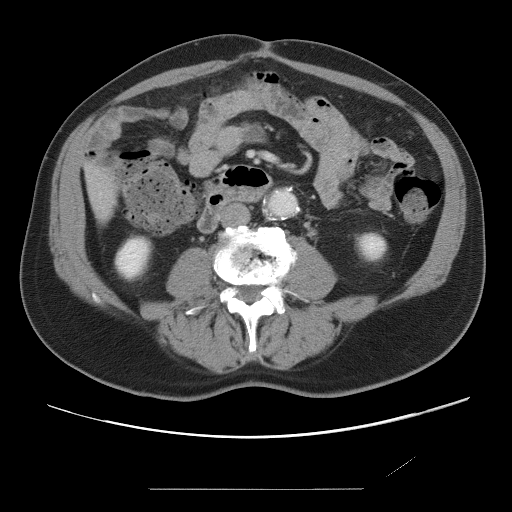
Contrast-enhanced abdominal CT, one axial slice. Position 9 of 87 along the scan axis. 120 kVp. Intravenous contrast given. Soft-tissue window (W 400 / L 40 HU). 5 mm slice thickness. 512 × 512 image matrix, field of view 406 × 406 mm. Male patient, age 74 years. From the clinical record (not read from this slice): diagnosis: colorectal cancer liver metastases, imaged before liver resection; multiple liver metastases: yes; largest metastasis: 1.1 cm.
Annotated regions visible in this slice (expert manual segmentation):
- liver: bounding box (x1, y1, x2, y2) in pixels: (88, 170, 115, 219)
- planned liver remnant (the part of the liver to remain after resection): (88, 170, 115, 219)